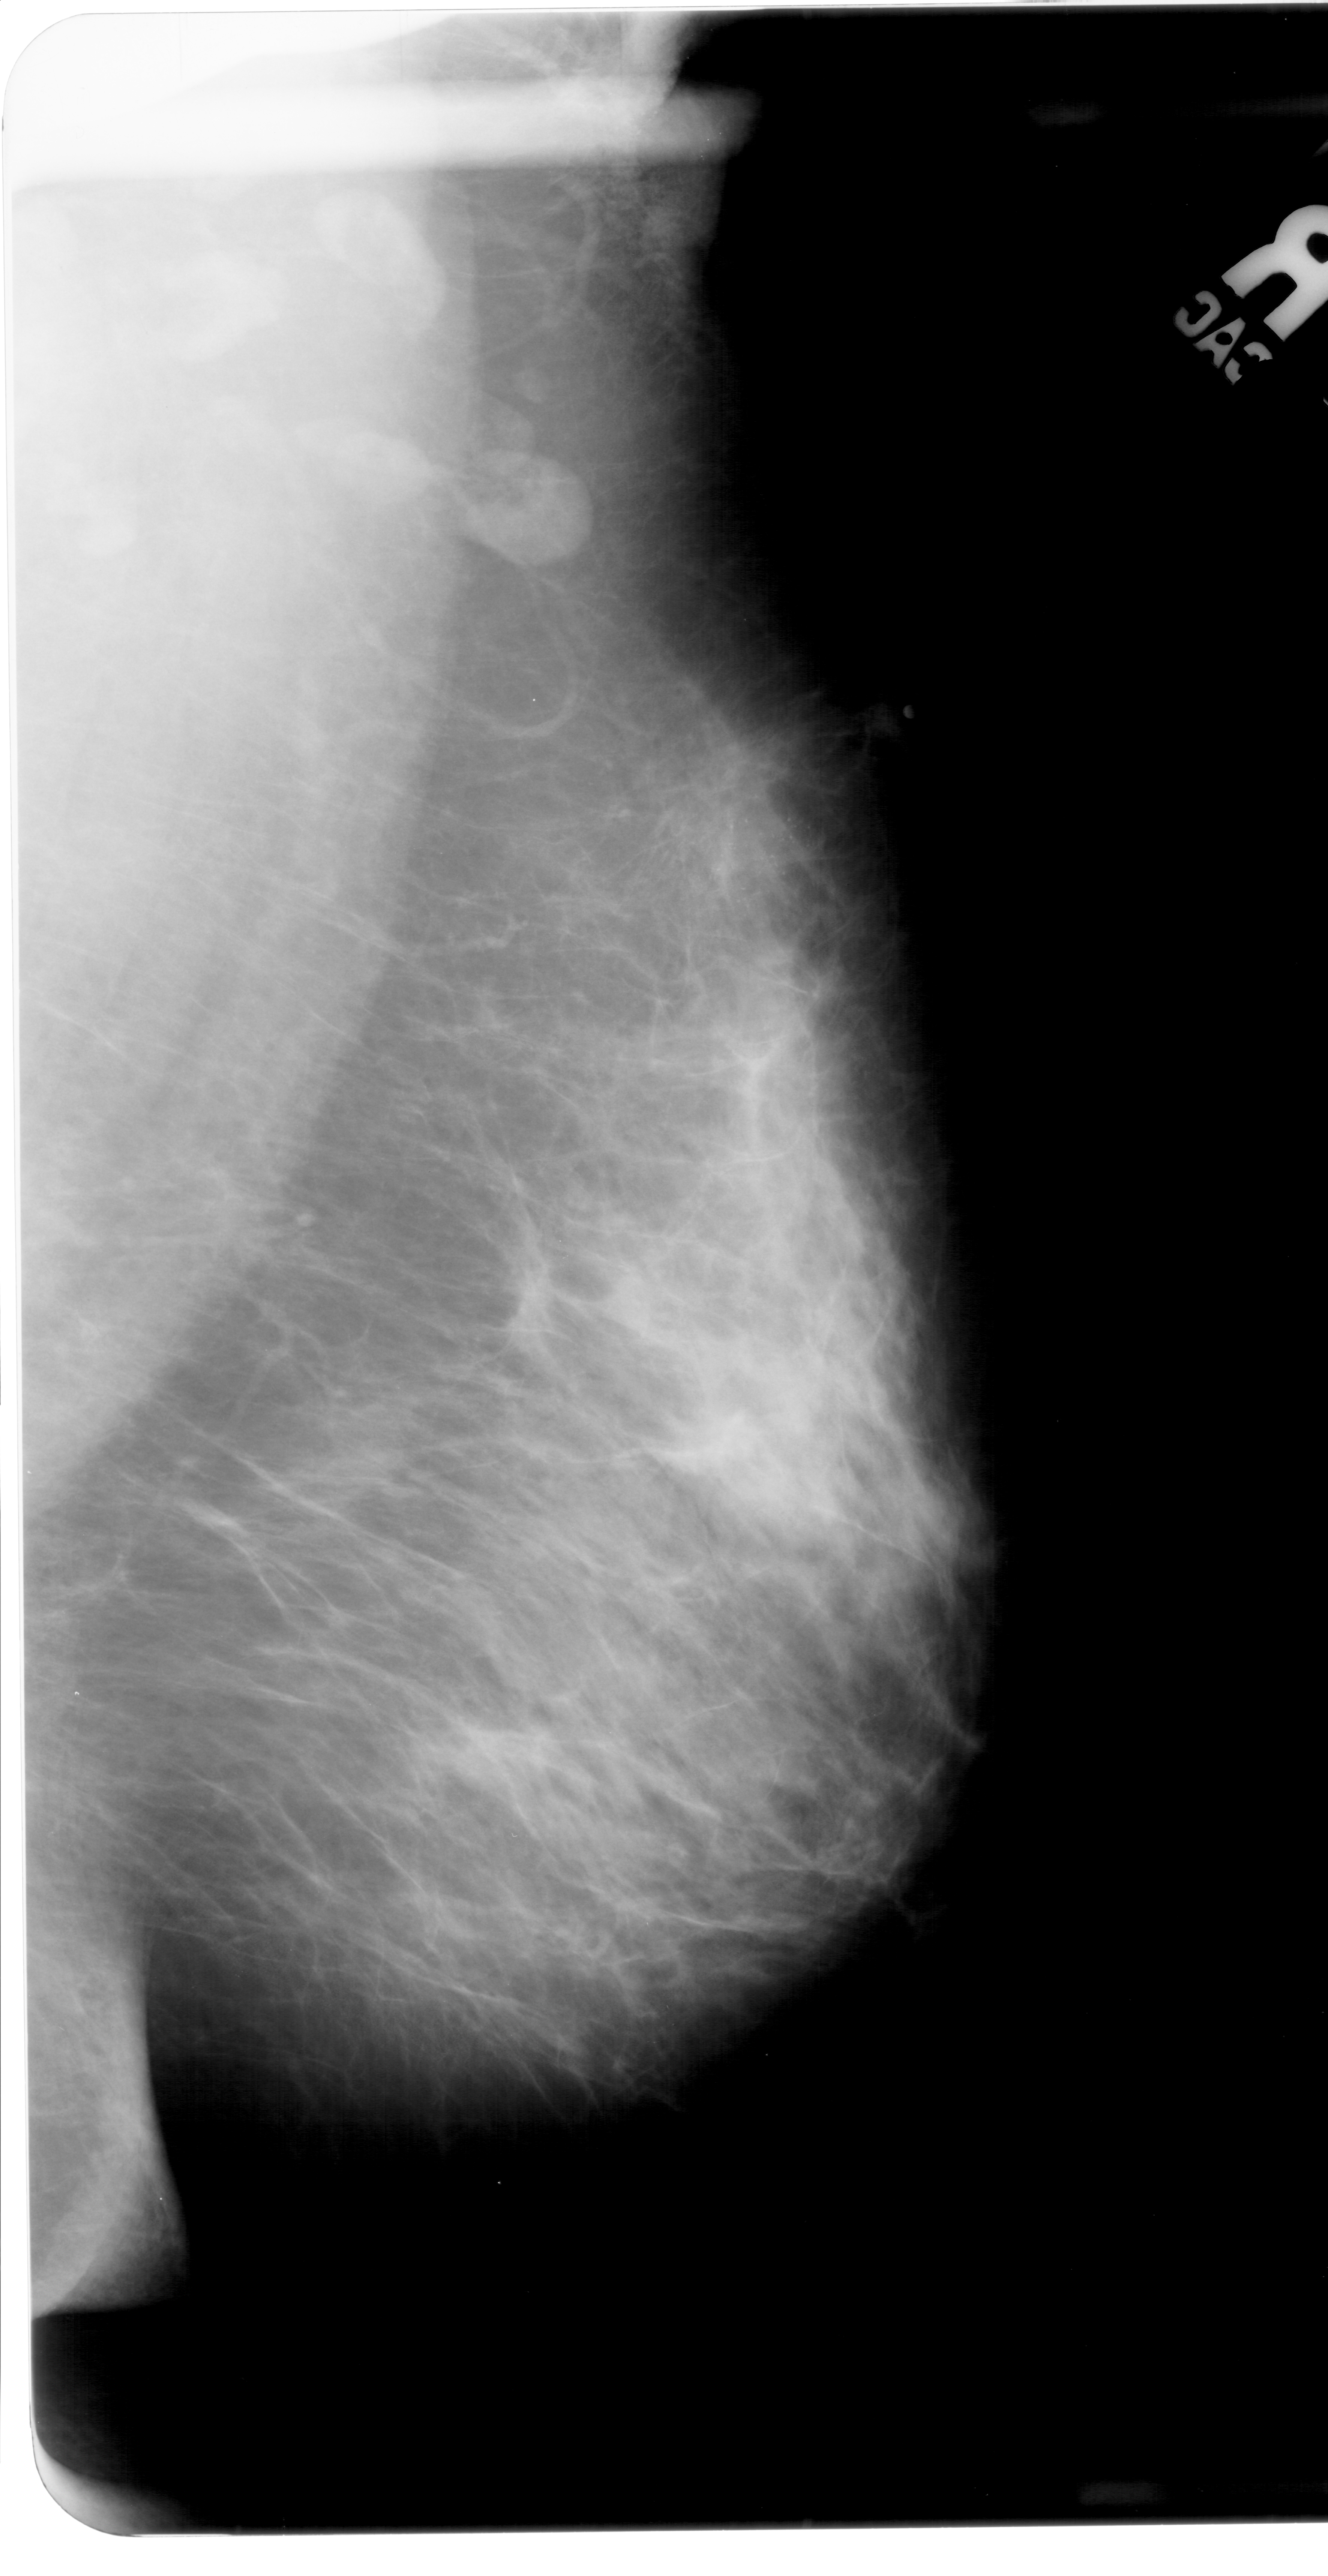
Mammogram (digitized film), right breast, mediolateral oblique (MLO) view, breast composition: heterogeneously dense (BI-RADS density category 3 of 4).
Calcifications, morphology pleomorphic, distribution clustered; BI-RADS assessment category 4; pathology (as recorded): malignant.